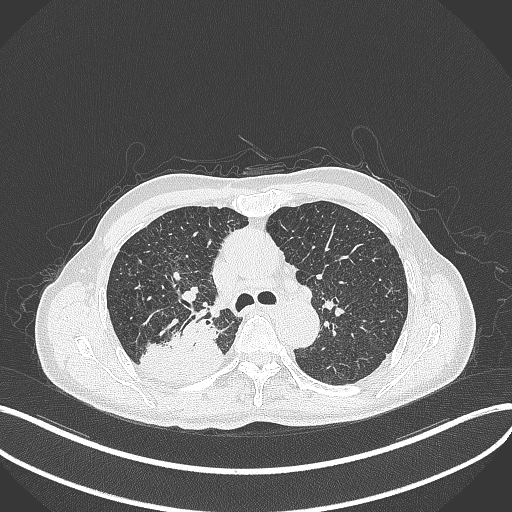
Chest CT, one axial slice. Position 304 of 428 along the scan axis. Reconstruction kernel B70f. 120 kVp. Lung window (W 1500 / L -600 HU). 512 × 512 image matrix. Patient: male, 79 years. Case-level facts recorded for this patient, not image findings: clinical TNM (as recorded): T3 N0 M0.
Outlined on this slice (rectangle marked by the reading radiologist):
- lung tumour (recorded histology: adenocarcinoma): box from (x=139, y=309) to (x=224, y=384) px